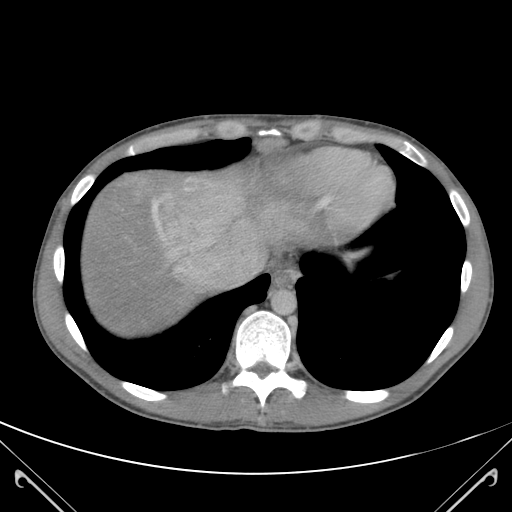
Contrast-enhanced abdominal CT (liver protocol), one axial slice. Slice 104 of 118 in the series (ordered by position). 120 kVp. Soft-tissue window (W 400 / L 40 HU). 3 mm slice thickness. 512 × 512 image matrix, field of view 380 × 380 mm. Case-level facts recorded for this patient, not image findings: diagnosis: hepatocellular carcinoma (patient treated with transarterial chemoembolisation; whether this scan precedes or follows treatment is not stated here); TNM stage (as recorded): Stage-IIIB; Child-Pugh class: A.
Outlined on this slice (semi-automatic segmentation, software-assisted and operator-edited):
- abdominal aorta: box from (x=273, y=290) to (x=296, y=313) px
- liver parenchyma outside the tumour (the mass and vessels are separate outlines, so this box may not span the whole liver): (x=82, y=164)–(x=287, y=332)
- mass: (x=159, y=179)–(x=245, y=252)
- liver vessels: (x=152, y=178)–(x=256, y=283)